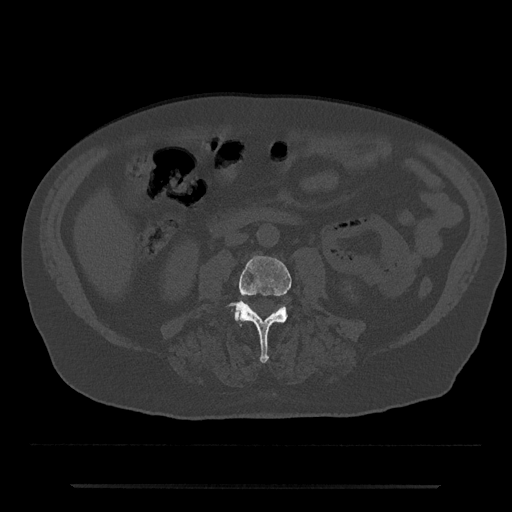
CT including the spine, one axial slice. Slice 402 of 797 in the series (ordered by position). 120 kVp. Bone window (W 1800 / L 400 HU). 0.5 mm slice thickness. 512 × 512 image matrix. Male patient, age 80 years. Case-level facts recorded for this patient, not image findings: primary cancer: prostate; vertebrae with lytic lesions (as recorded): L1, T11.
Annotated regions visible in this slice (semi-automatic segmentation, software-assisted and operator-edited):
- L3 vertebra: bounding box [x1, y1, x2, y2] px = [230, 256, 292, 363]
- L4 vertebra: [234, 306, 284, 321]